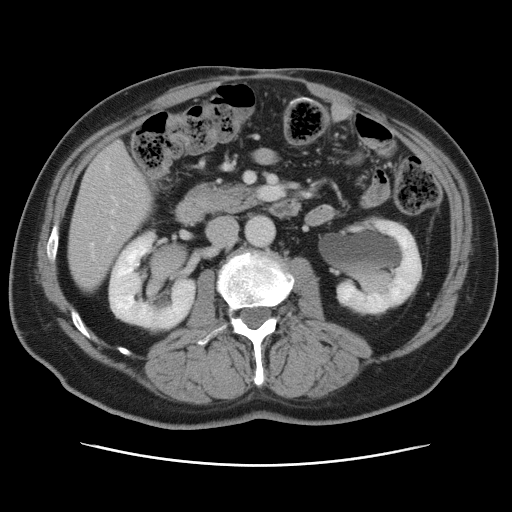
Contrast-enhanced abdominal CT, one axial slice. Position 26 of 80 along the scan axis. Soft-tissue window (W 400 / L 40 HU). 5 mm slice thickness. 512 × 512 image matrix. Male patient, age 69 years. Case-level facts recorded for this patient, not image findings: diagnosis: colorectal cancer liver metastases, imaged before liver resection; multiple liver metastases: no; largest metastasis: 5 cm; disease in both lobes: yes.
Annotated regions visible in this slice (manually delineated by an expert):
- hepatic veins: bounding box [x1, y1, x2, y2] px = [90, 166, 117, 248]
- liver: [69, 144, 152, 291]
- planned liver remnant (the part of the liver to remain after resection): [69, 219, 131, 291]